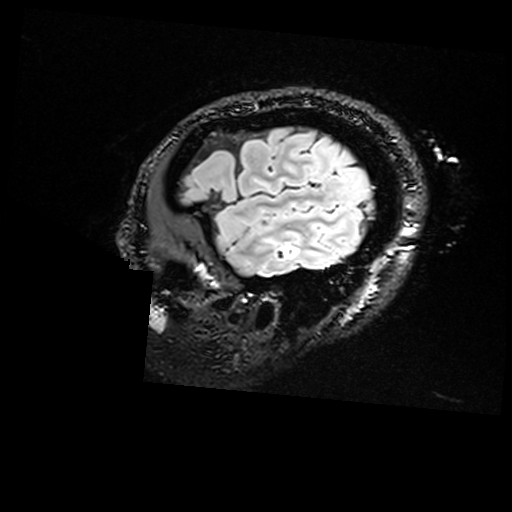
Brain MRI from a brain-tumour surgery series, one sagittal slice. Position 139 of 176 along the scan axis. T2 FLAIR. 1 mm slice thickness. 512 × 512 image matrix. From the clinical record (not read from this slice): histopathology: Non-tumor destructive chronic inflammatory lesion with abnormal vasculature; tumour location: Right Inferior Temporal.
Outlined on this slice (outlined manually by an expert reader):
- residual tumour: bounding box [x1, y1, x2, y2] px = [285, 244, 291, 259]